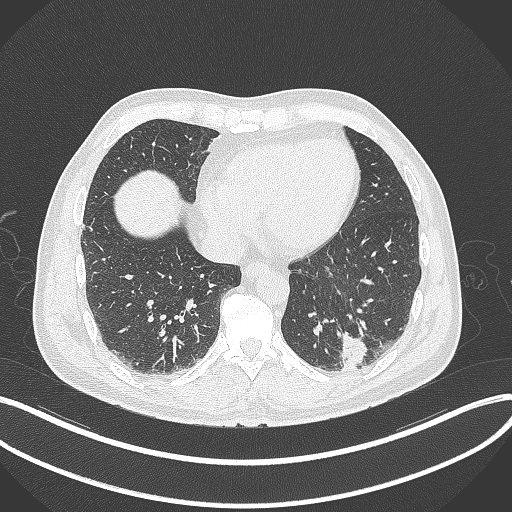
Chest CT, one axial slice. Position 85 of 300 along the scan axis. Reconstruction kernel B70f. 120 kVp. Lung window (W 1500 / L -600 HU). 1 mm slice thickness. 512 × 512 image matrix, field of view 400 × 400 mm. Male patient, age 54 years. From the clinical record (not read from this slice): clinical TNM (as recorded): T1c N0 M1.
Annotated regions visible in this slice (rectangle marked by the reading radiologist):
- lung tumour (recorded histology: adenocarcinoma): bounding box (x1, y1, x2, y2) in pixels: (336, 327, 373, 378)